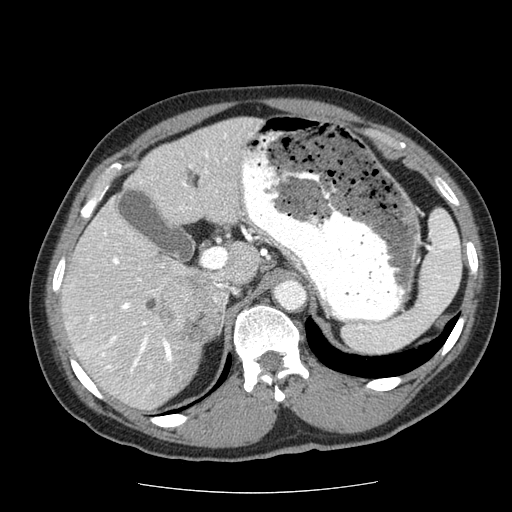
Contrast-enhanced abdominal CT (liver protocol), one axial slice. Slice 35 of 85 in the series (ordered by position). Soft-tissue window (W 400 / L 40 HU). 512 × 512 image matrix, field of view 360 × 360 mm. Case-level facts recorded for this patient, not image findings: diagnosis: hepatocellular carcinoma (patient treated with transarterial chemoembolisation; whether this scan precedes or follows treatment is not stated here); TNM stage (as recorded): Stage-IIIA; Child-Pugh class: A; tumour size: 8 cm.
Outlined on this slice (semi-automatically segmented with operator editing):
- abdominal aorta: bounding box [x1, y1, x2, y2] px = [277, 280, 305, 308]
- liver parenchyma outside the tumour (the mass and vessels are separate outlines, so this box may not span the whole liver): [62, 116, 262, 410]
- mass: [143, 274, 223, 344]
- liver vessels: [77, 134, 227, 390]